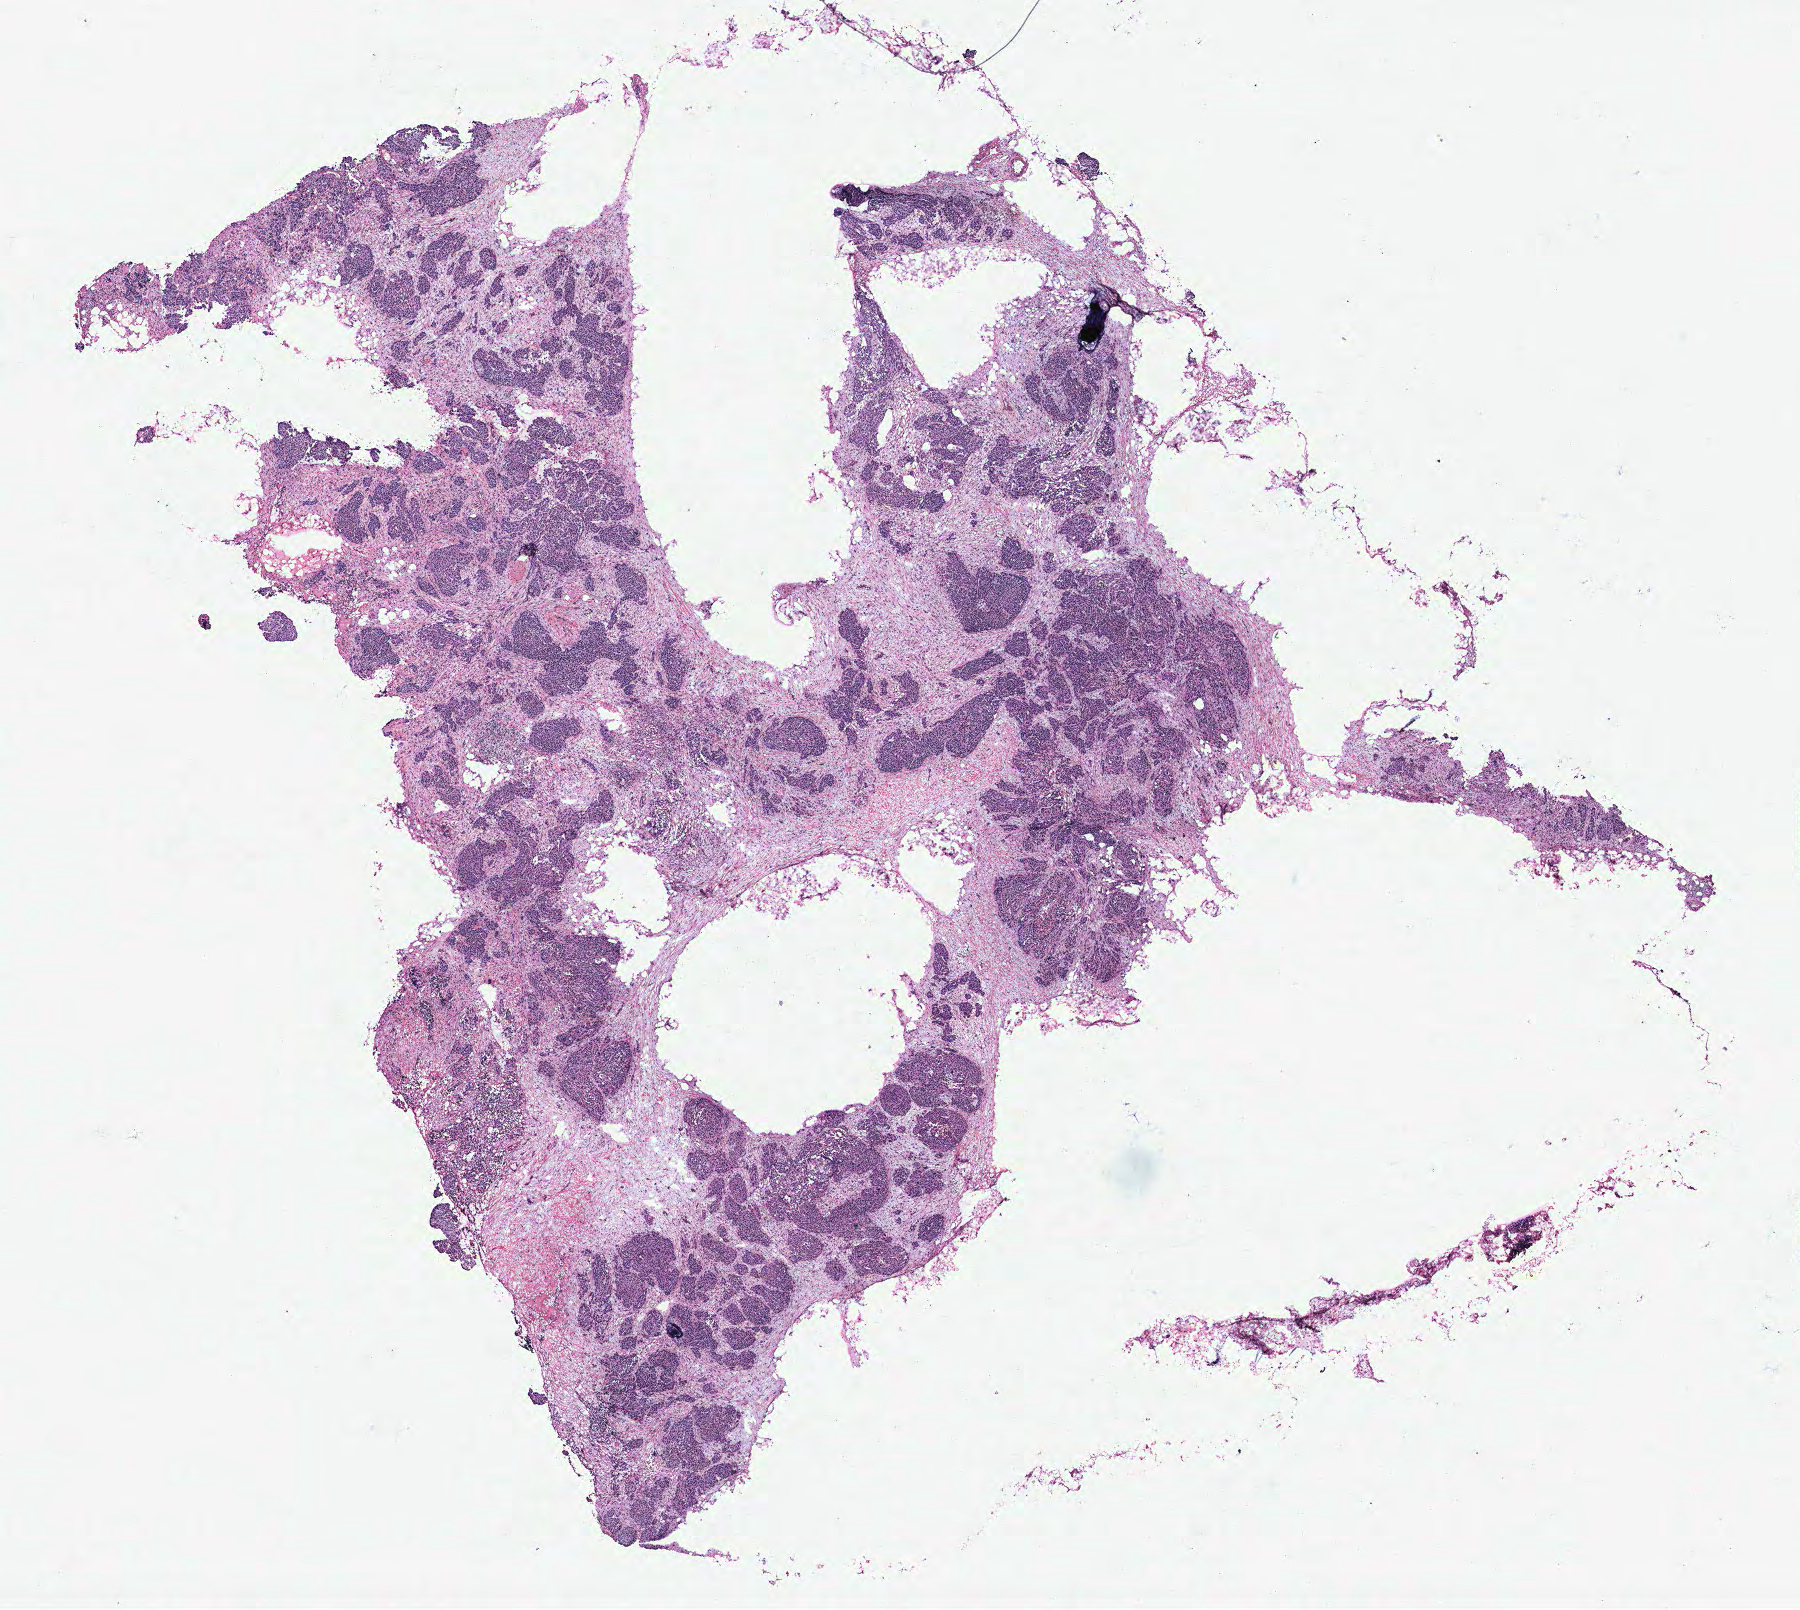
Digitized H&E tissue section (whole slide) — shown as a low-resolution overview of the whole scanned area (about 14.4 x 12.9 mm); ovary, tumour tissue. 63-year-old female patient.
Primary tumour site (as recorded): fallopian tube. Histologic diagnosis: Serous adenocarcinoma, NOS (fallopian tube).